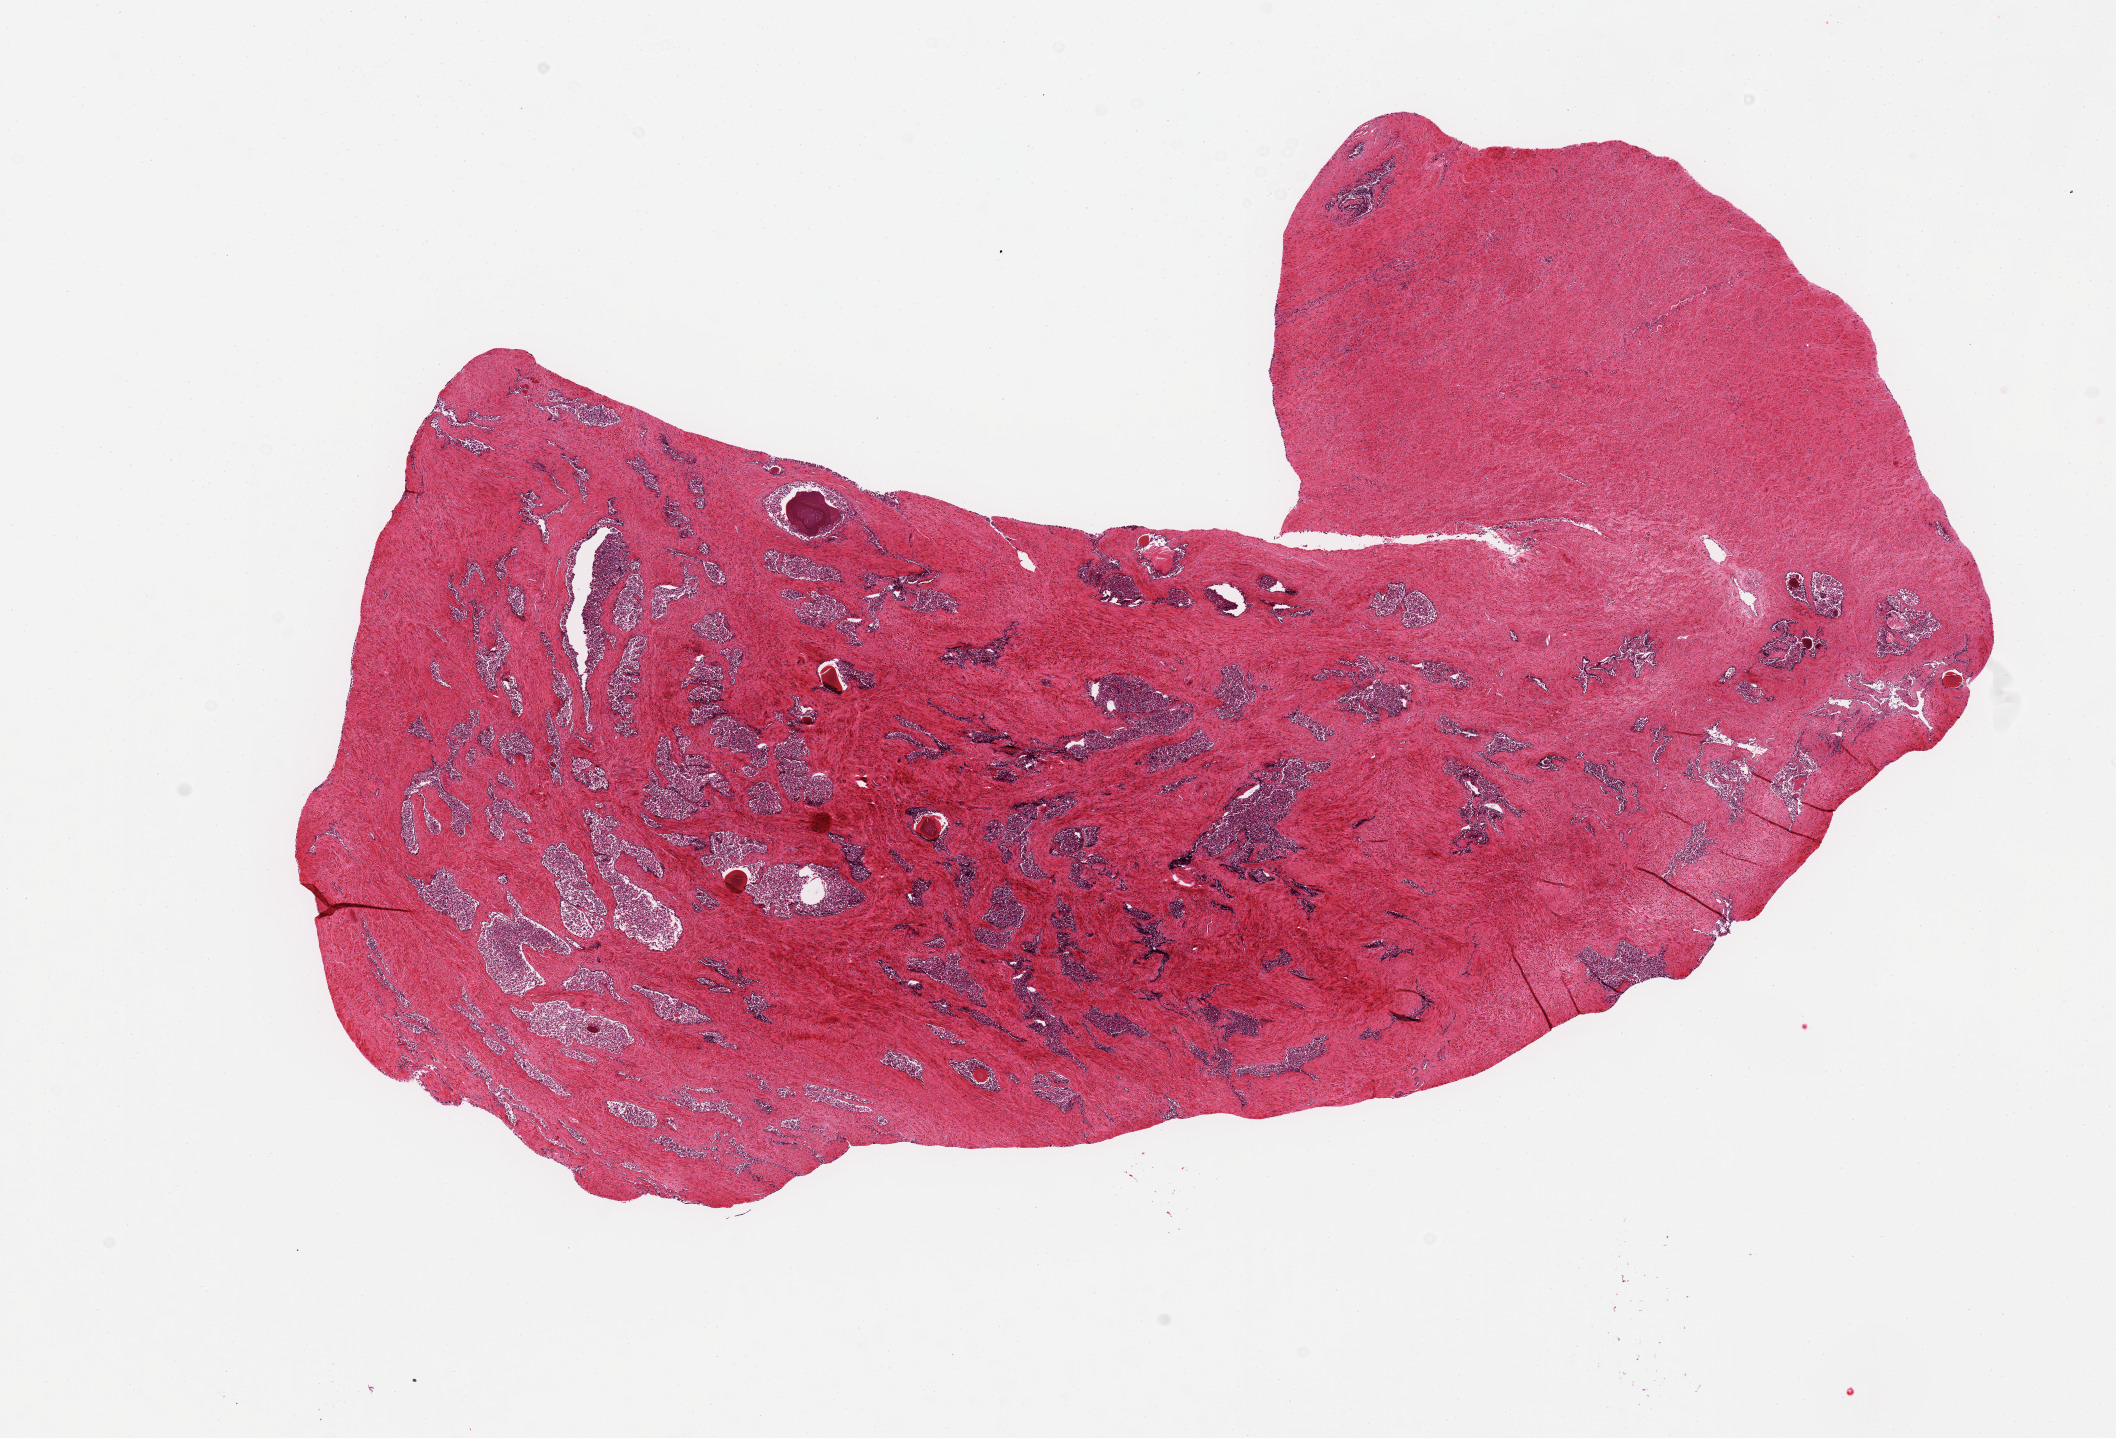
Whole-slide image, haematoxylin and eosin stain, low-resolution overview of the scanned area, about 16.7 x 11.4 mm (acquisition: 20x scan), PAXgene-fixed paraffin-embedded (PFPE) section, section of prostate (target tissue), tissue donor sample. Male donor.
* review note (as recorded): Severe glandular autolysis, but cells still identifiable